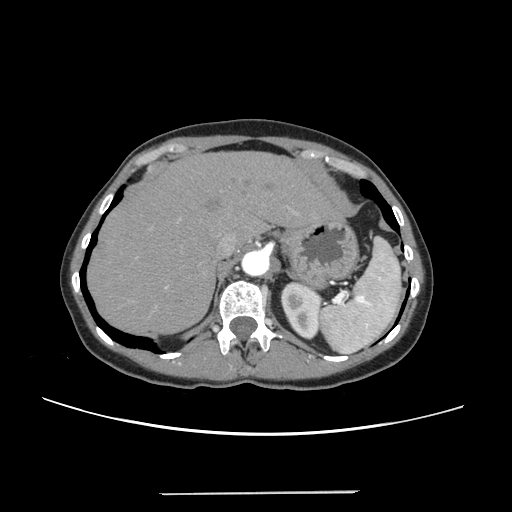
Contrast-enhanced abdominal CT, one axial slice; slice 188 of 240 in the series (ordered by position); 120 kVp; intravenous contrast given; soft-tissue window (W 400 / L 40 HU); 512 × 512 image matrix, field of view 371 × 371 mm. Female patient, age 60 years. Case-level facts recorded for this patient, not image findings: diagnosis: colorectal cancer liver metastases, imaged before liver resection; multiple liver metastases: no; largest metastasis: 1.5 cm; disease in both lobes: no.
Outlined on this slice (manually delineated by an expert):
- hepatic veins: box from (x=220, y=234) to (x=236, y=254) px
- liver: (x=89, y=153)–(x=336, y=335)
- planned liver remnant (the part of the liver to remain after resection): (x=89, y=153)–(x=335, y=335)
- portal vein (with intrahepatic branches): (x=136, y=219)–(x=180, y=288)